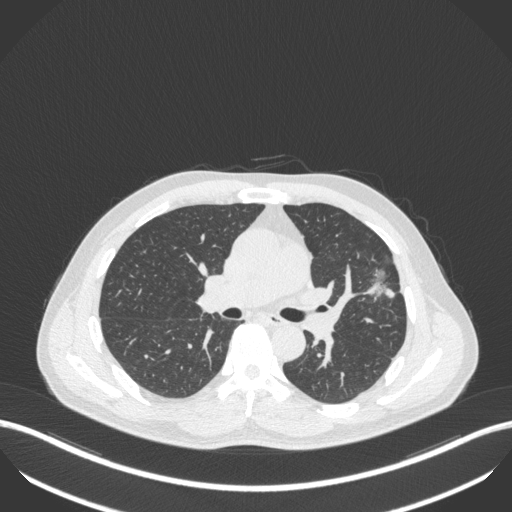
Chest CT, one axial slice; 120 kVp; lung window (W 1500 / L -600 HU); 1 mm slice thickness; 512 × 512 image matrix, field of view 400 × 400 mm. Patient: male, 55 years. From the clinical record (not read from this slice): clinical TNM (as recorded): T1c N0 M0.
Structures marked on this image (rectangle marked by the reading radiologist):
- lung tumour (recorded histology: adenocarcinoma): box from (x=358, y=268) to (x=401, y=304) px